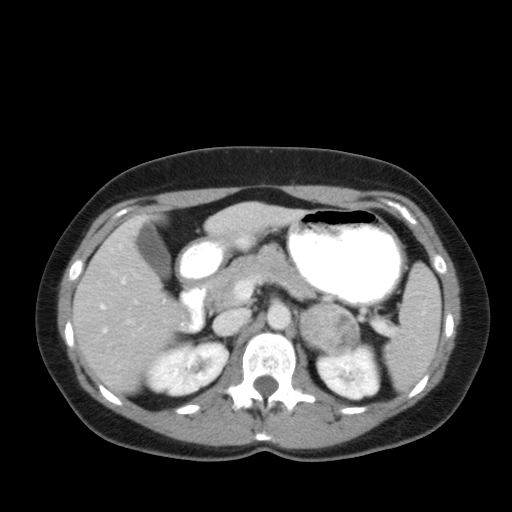
Contrast-enhanced abdominal CT, one axial slice; position 32 of 92 along the scan axis; 120 kVp; soft-tissue window (W 400 / L 40 HU); 5 mm slice thickness; 512 × 512 image matrix, field of view 369 × 369 mm. Patient: female, 35 years. Case-level facts recorded for this patient, not image findings: diagnosis: adrenocortical carcinoma; tumour side: left adrenal; tumour size at pathology: 6.6 cm; Ki-67 index: 5 %; stage (as recorded): 2.
Structures marked on this image (semi-automatically segmented with operator editing):
- mass: bounding box <301,302,357,353> (left, top, right, bottom; pixels)